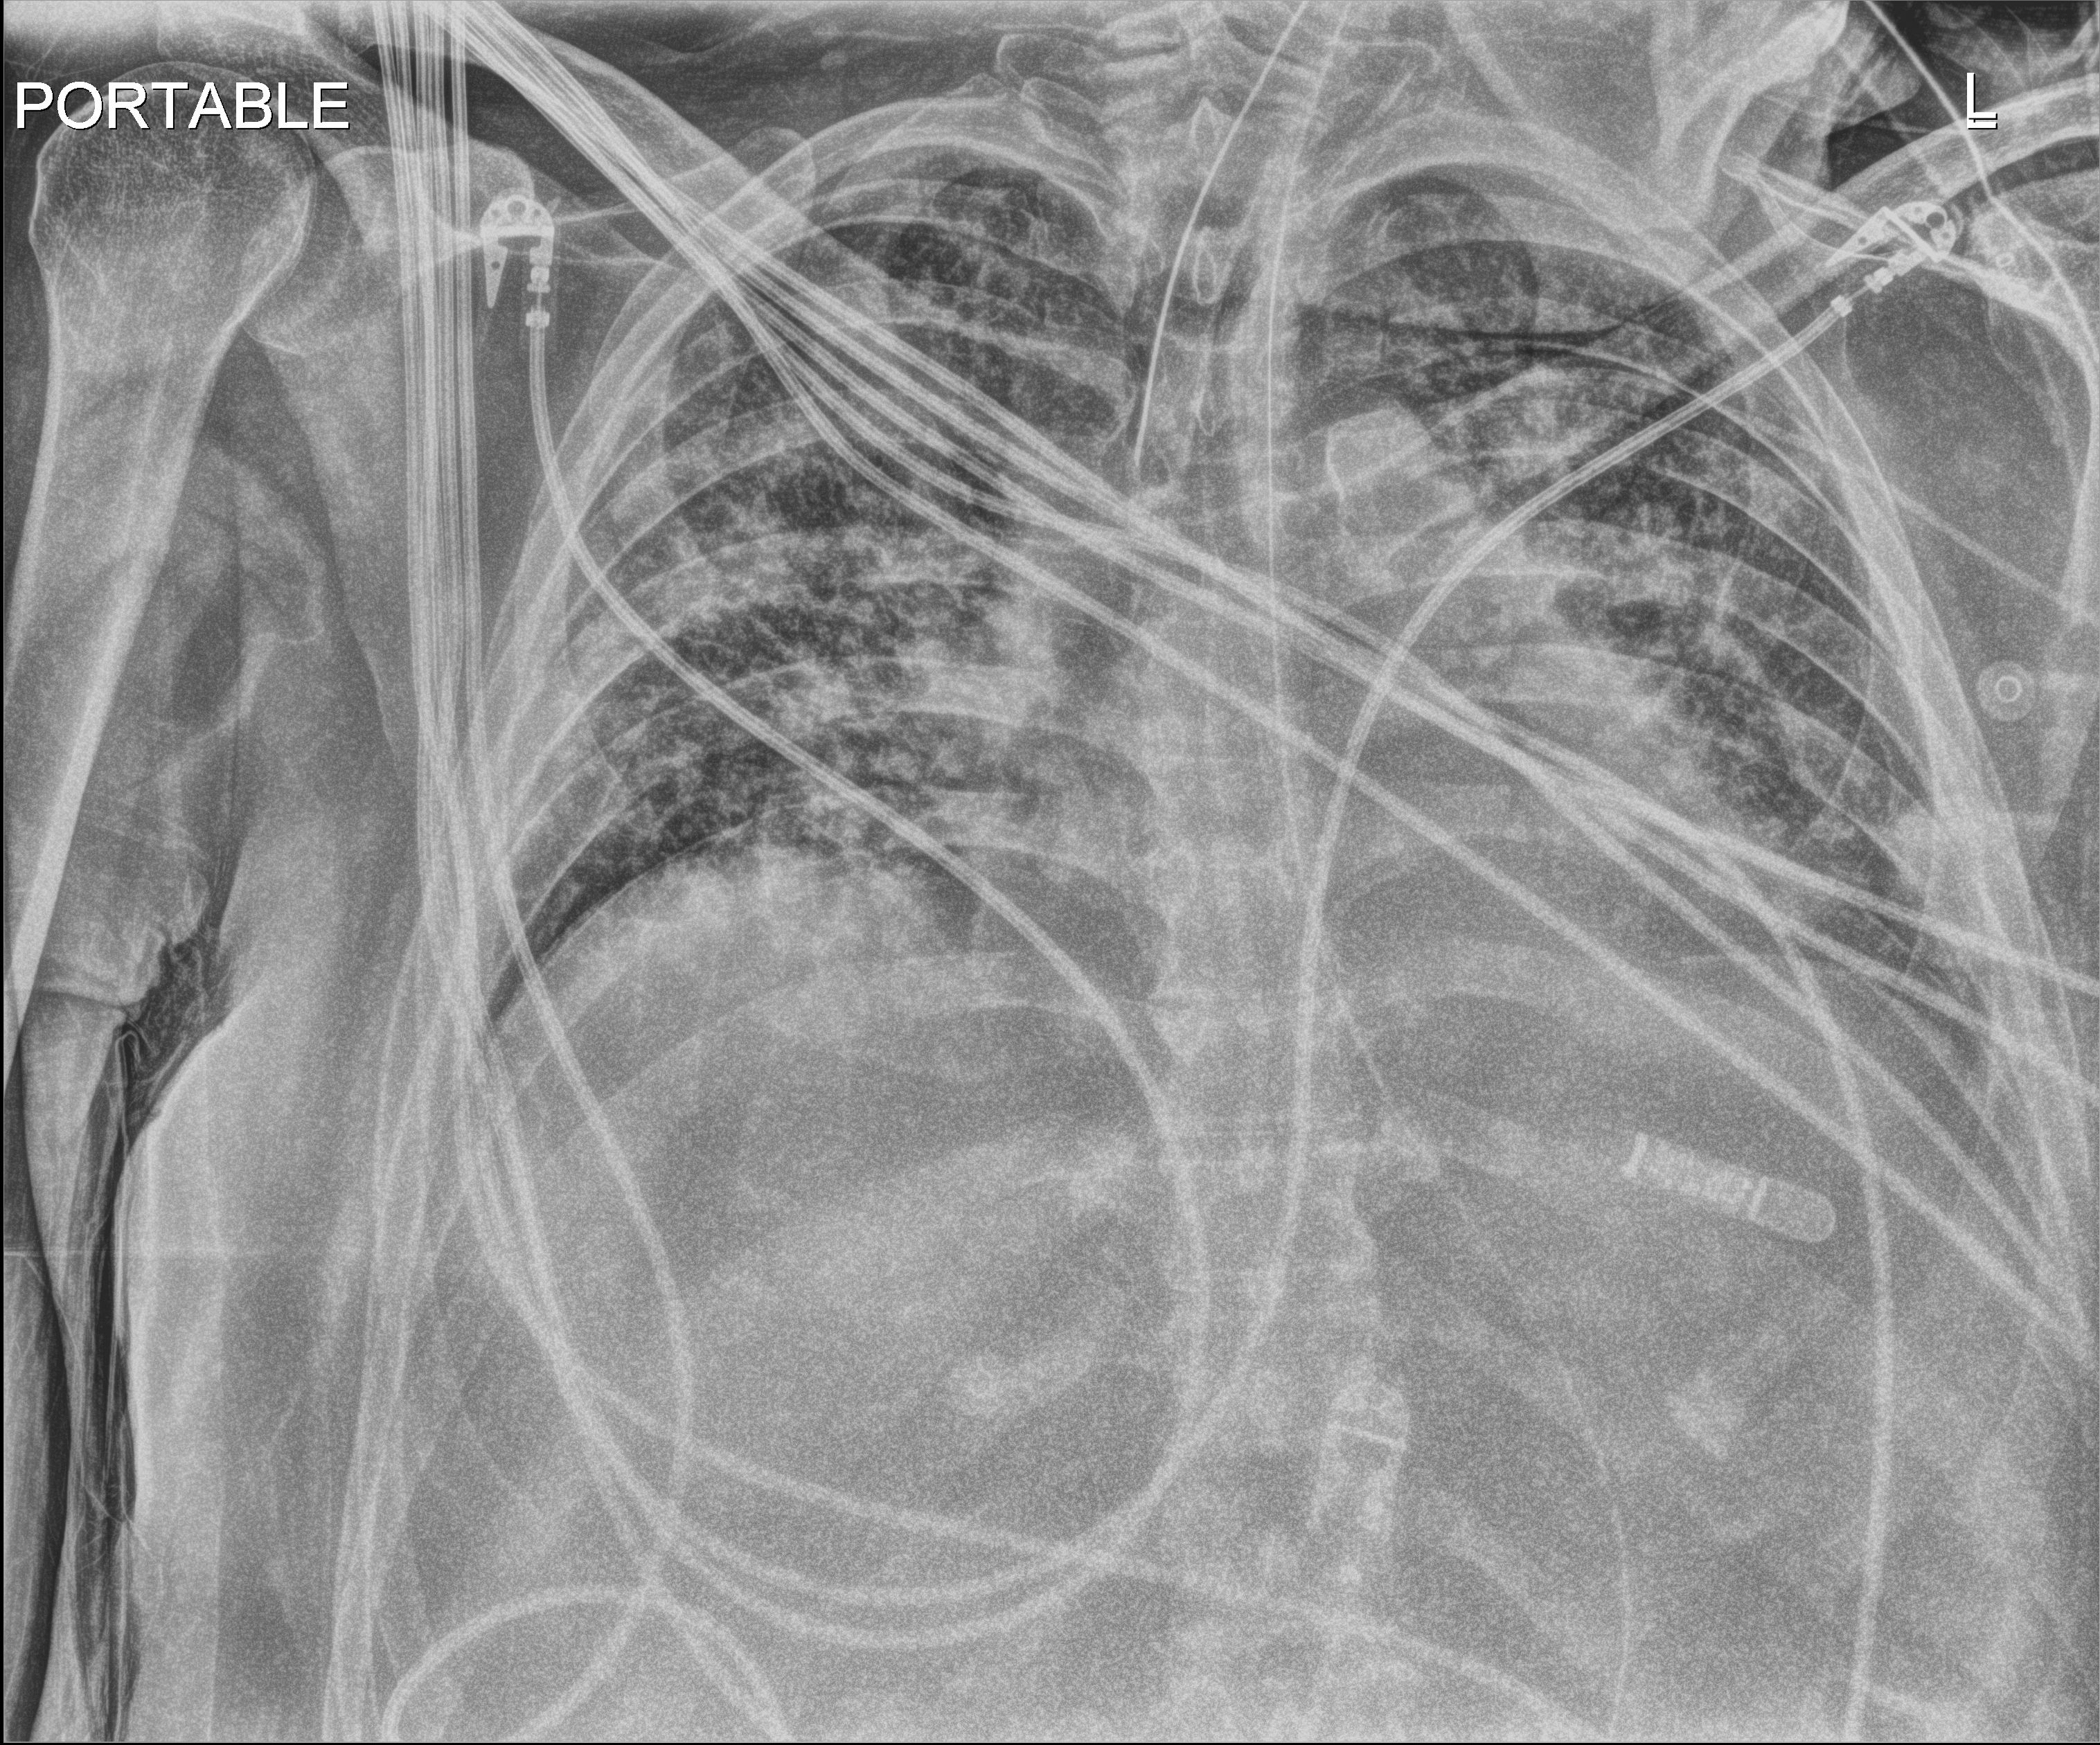
Chest X-ray (portable), anteroposterior (AP) projection. Male patient hospitalised with COVID-19, age 18–59 years.
Admission-level facts for this patient (not findings on this image; timing relative to this image not recorded): admitted to intensive care during this hospital stay: yes; length of hospital stay: 39 days.